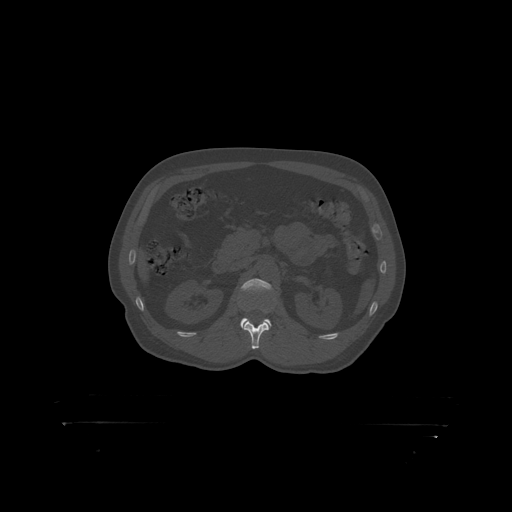
CT including the spine, one axial slice; position 313 of 399 along the scan axis; bone window (W 1800 / L 400 HU); 1.25 mm slice thickness; 512 × 512 image matrix, field of view 650 × 650 mm. Patient: male, 46 years. Case-level facts recorded for this patient, not image findings: primary cancer: skin.
Outlined on this slice (semi-automatically segmented with operator editing):
- L2 vertebra: bounding box <241,279,274,293> (left, top, right, bottom; pixels)